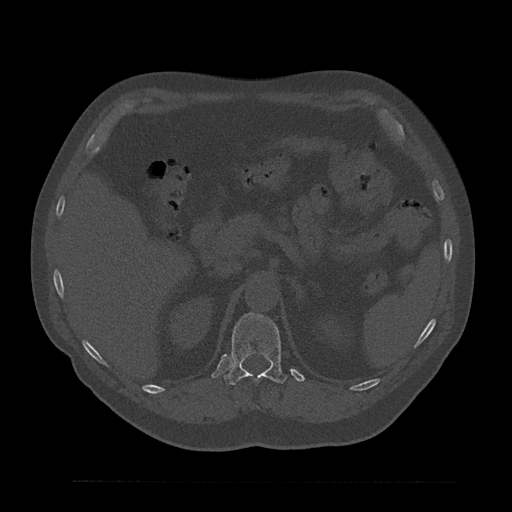
CT including the spine, one axial slice; bone window (W 1800 / L 400 HU); 512 × 512 image matrix, field of view 430 × 430 mm. Male patient, age 61 years. From the clinical record (not read from this slice): primary cancer: prostate.
Structures marked on this image (semi-automatic segmentation, software-assisted and operator-edited):
- T12 vertebra: bounding box [x1, y1, x2, y2] px = [224, 313, 287, 386]